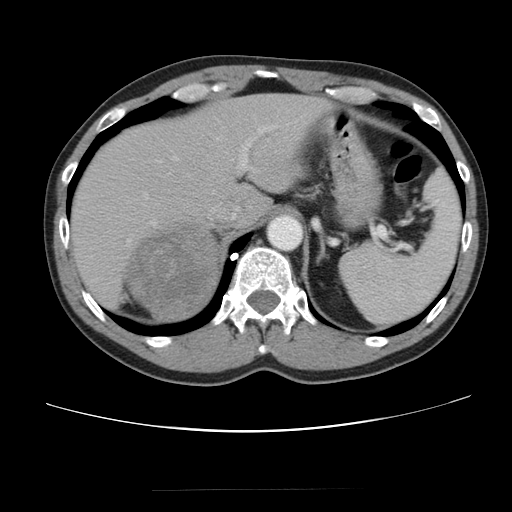
Contrast-enhanced abdominal CT, one axial slice. Position 69 of 80 along the scan axis. 120 kVp. Intravenous contrast given. Soft-tissue window (W 400 / L 40 HU). 5 mm slice thickness. 512 × 512 image matrix, field of view 360 × 360 mm. Patient: male, 61 years. From the clinical record (not read from this slice): diagnosis: adrenocortical carcinoma; tumour side: right adrenal; tumour size at pathology: 11.1 cm.
Outlined on this slice (semi-automatic segmentation, software-assisted and operator-edited):
- mass: bounding box <127,224,217,319> (left, top, right, bottom; pixels)